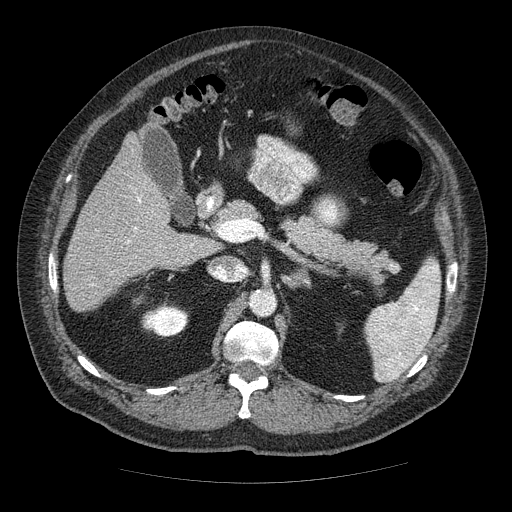
Contrast-enhanced abdominal CT (liver protocol), one axial slice; slice 25 of 85 in the series (ordered by position); reconstruction kernel STANDARD; soft-tissue window (W 400 / L 40 HU); 2.5 mm slice thickness; 512 × 512 image matrix, field of view 420 × 420 mm. Case-level facts recorded for this patient, not image findings: diagnosis: hepatocellular carcinoma (patient treated with transarterial chemoembolisation; whether this scan precedes or follows treatment is not stated here); TNM stage (as recorded): Stage-IIIA; Child-Pugh class: A; tumour nodularity: multinodular; tumour size: 7 cm.
Outlined on this slice (semi-automatic segmentation, software-assisted and operator-edited):
- liver parenchyma outside the tumour (the mass and vessels are separate outlines, so this box may not span the whole liver): bounding box (x1, y1, x2, y2) in pixels: (64, 132, 214, 310)
- liver vessels: (92, 197, 193, 285)